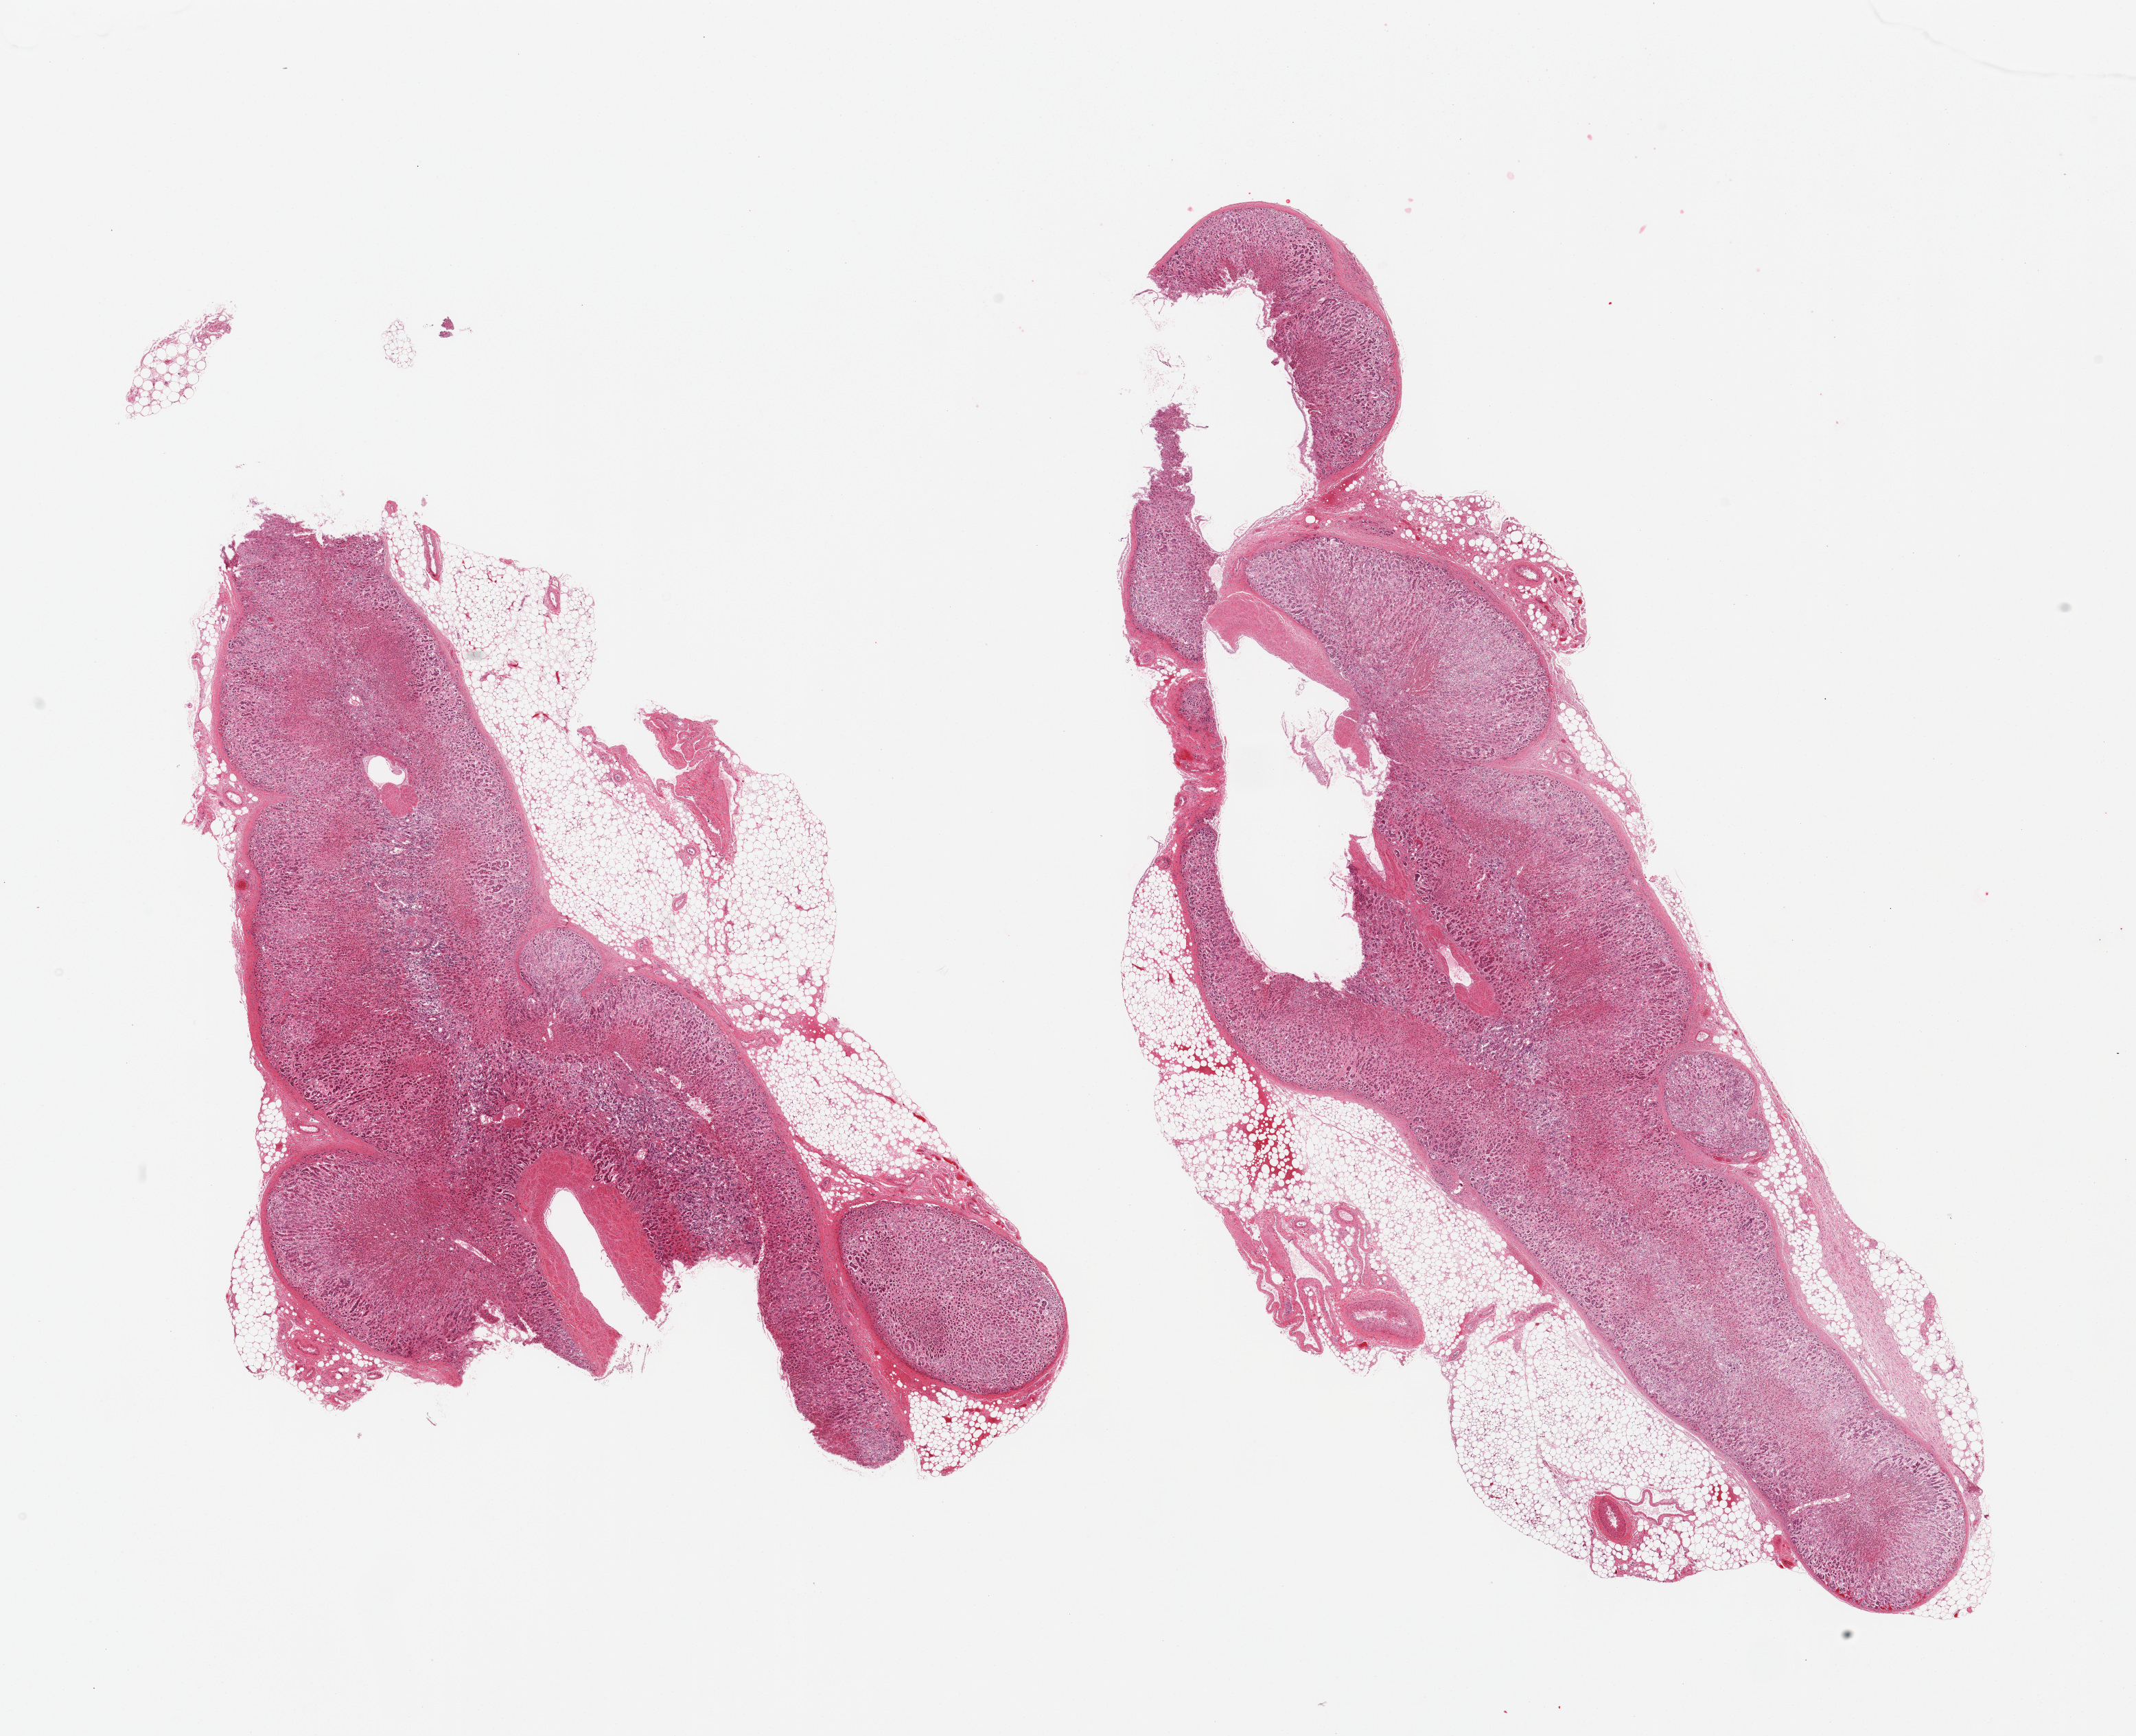
Whole-slide image, hematoxylin and eosin (H&E) stain — whole scanned area (about 24.6 x 20.0 mm, slide scanned at 20x) shown as a low-resolution overview; PAXgene-fixed, paraffin-embedded tissue; target tissue: adrenal gland; tissue donor sample. Donor sex: female.
* reviewer comment on this tissue sample: 2 pieces; both with ~25% attached fat